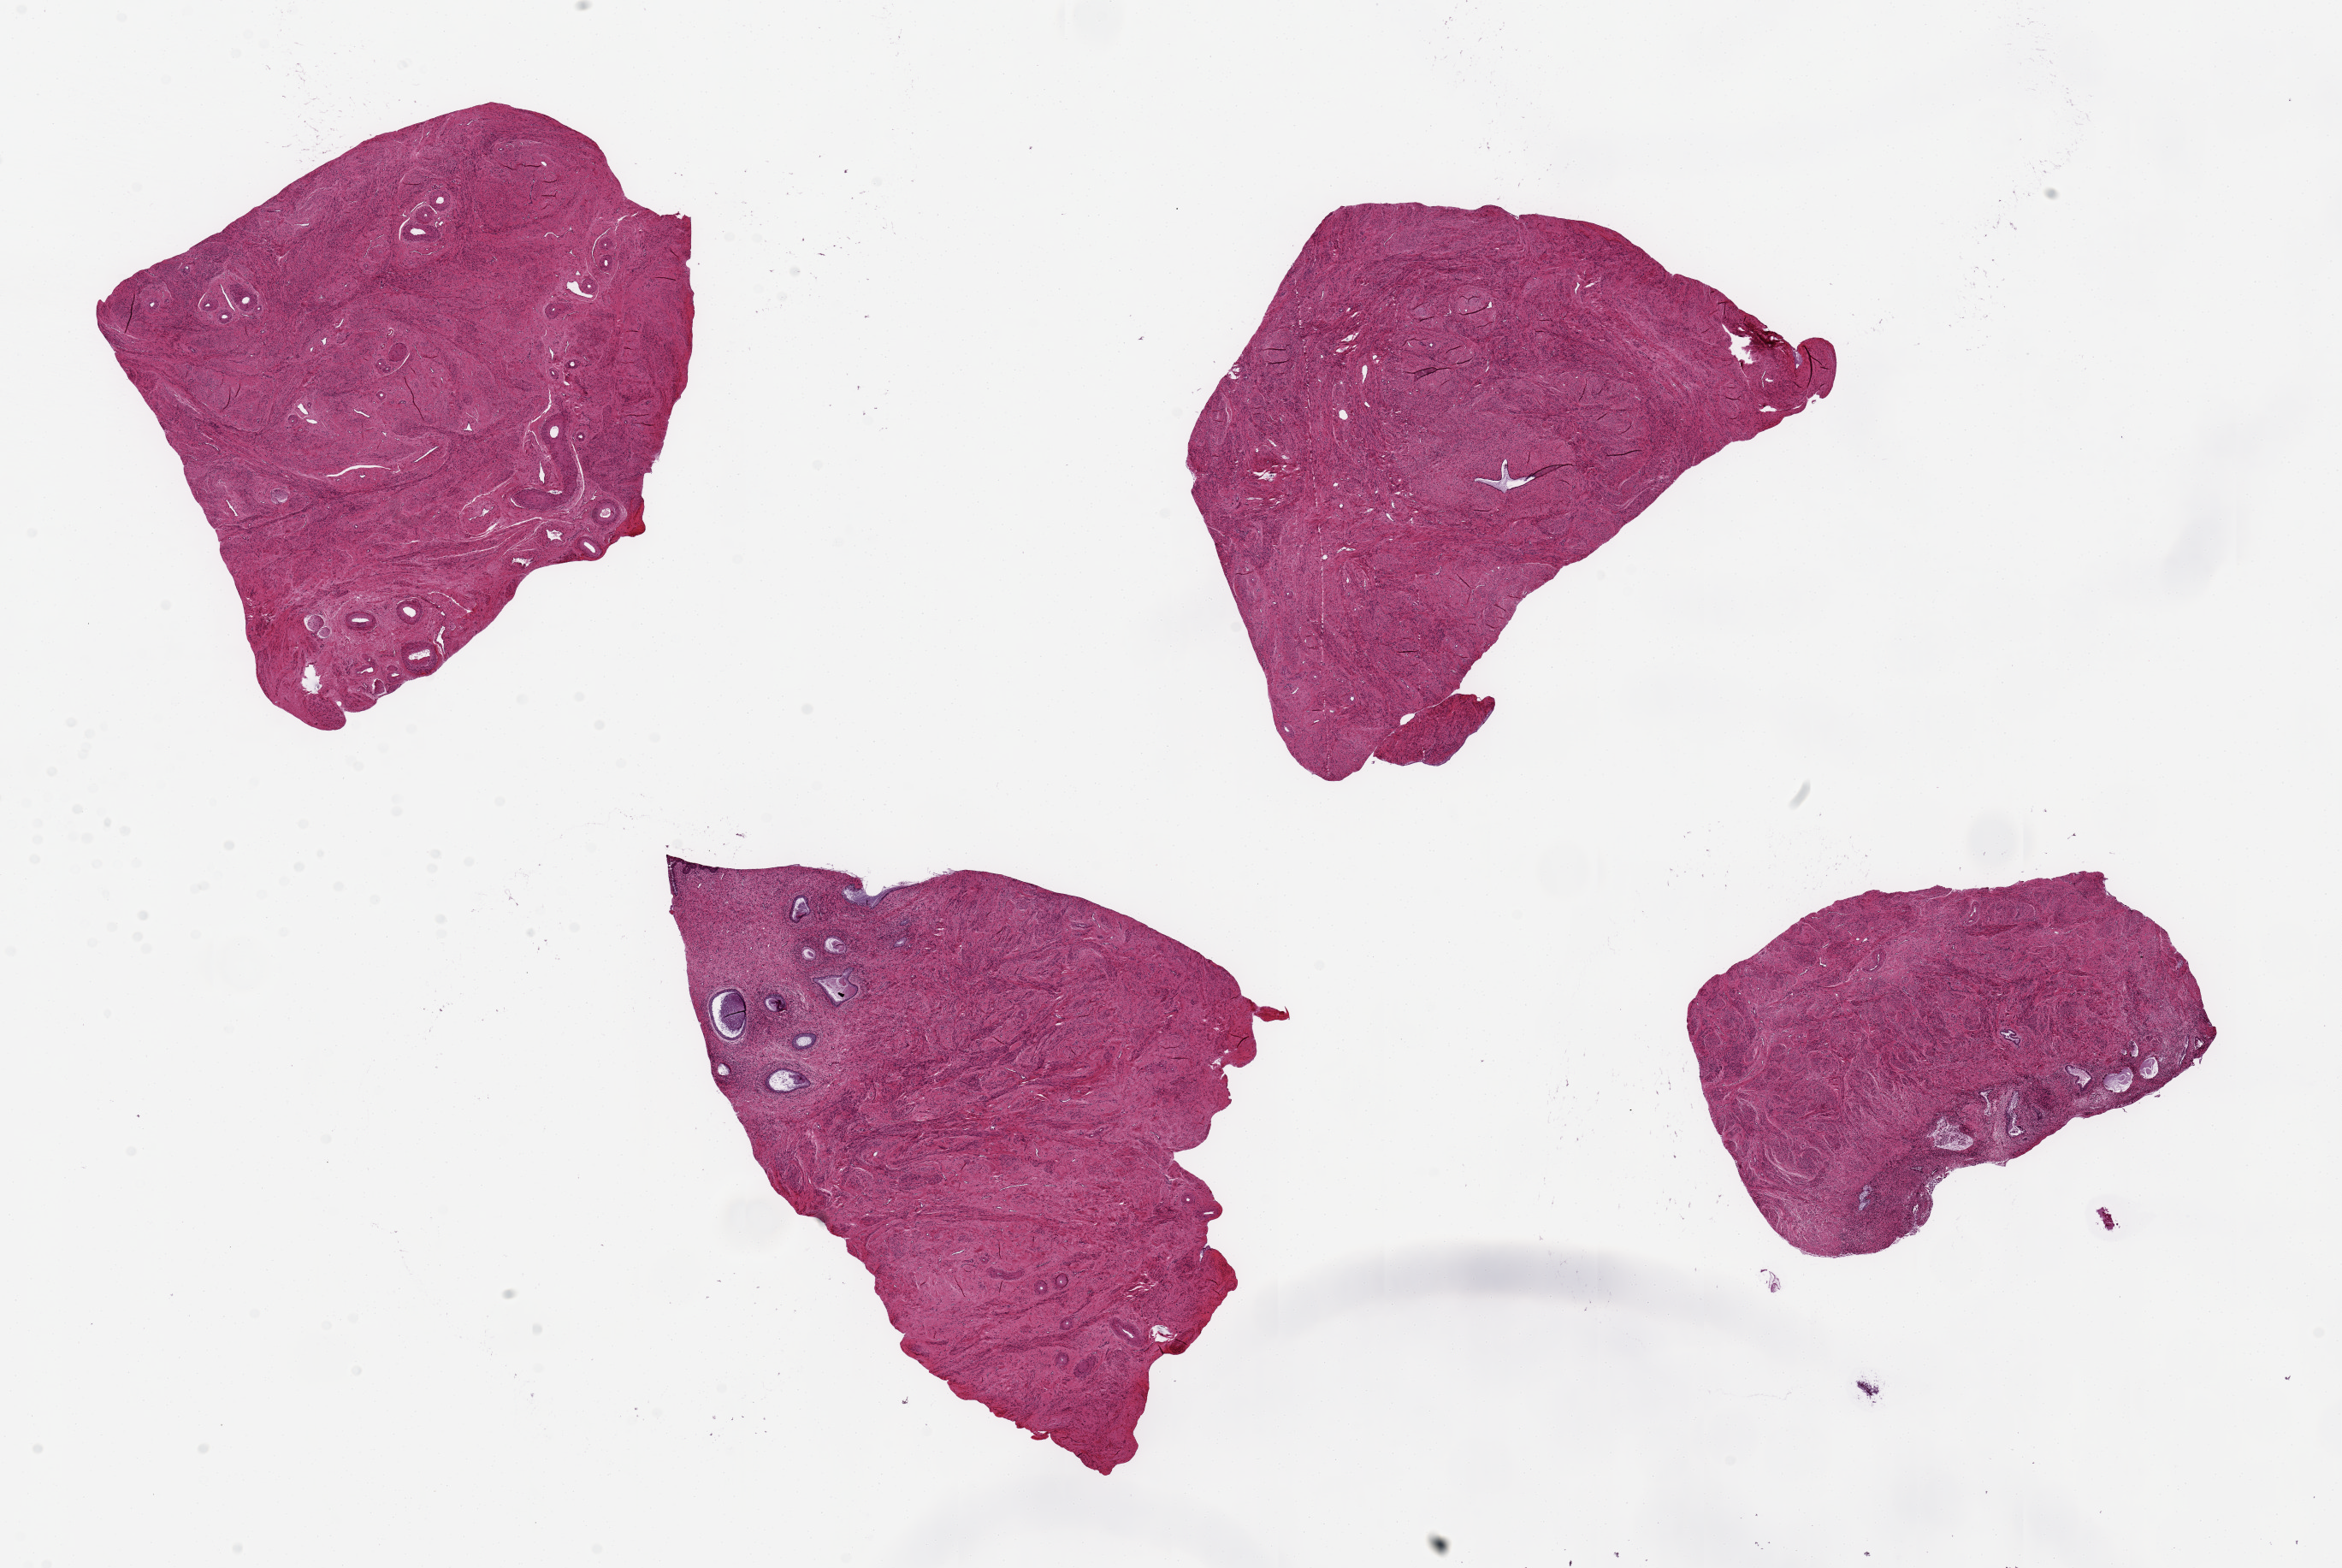
Whole-slide image, H&E stain, whole scanned area (about 21.7 x 14.5 mm, from a 20x scan) shown as a low-resolution overview, PAXgene-fixed paraffin-embedded (PFPE) section, sampled site (target tissue): endocervix, tissue donor sample. Donor: female.
Pathologist's review note for this sample: 4 pieces up to ~6x4.5 mm; 2 have apparent glands.